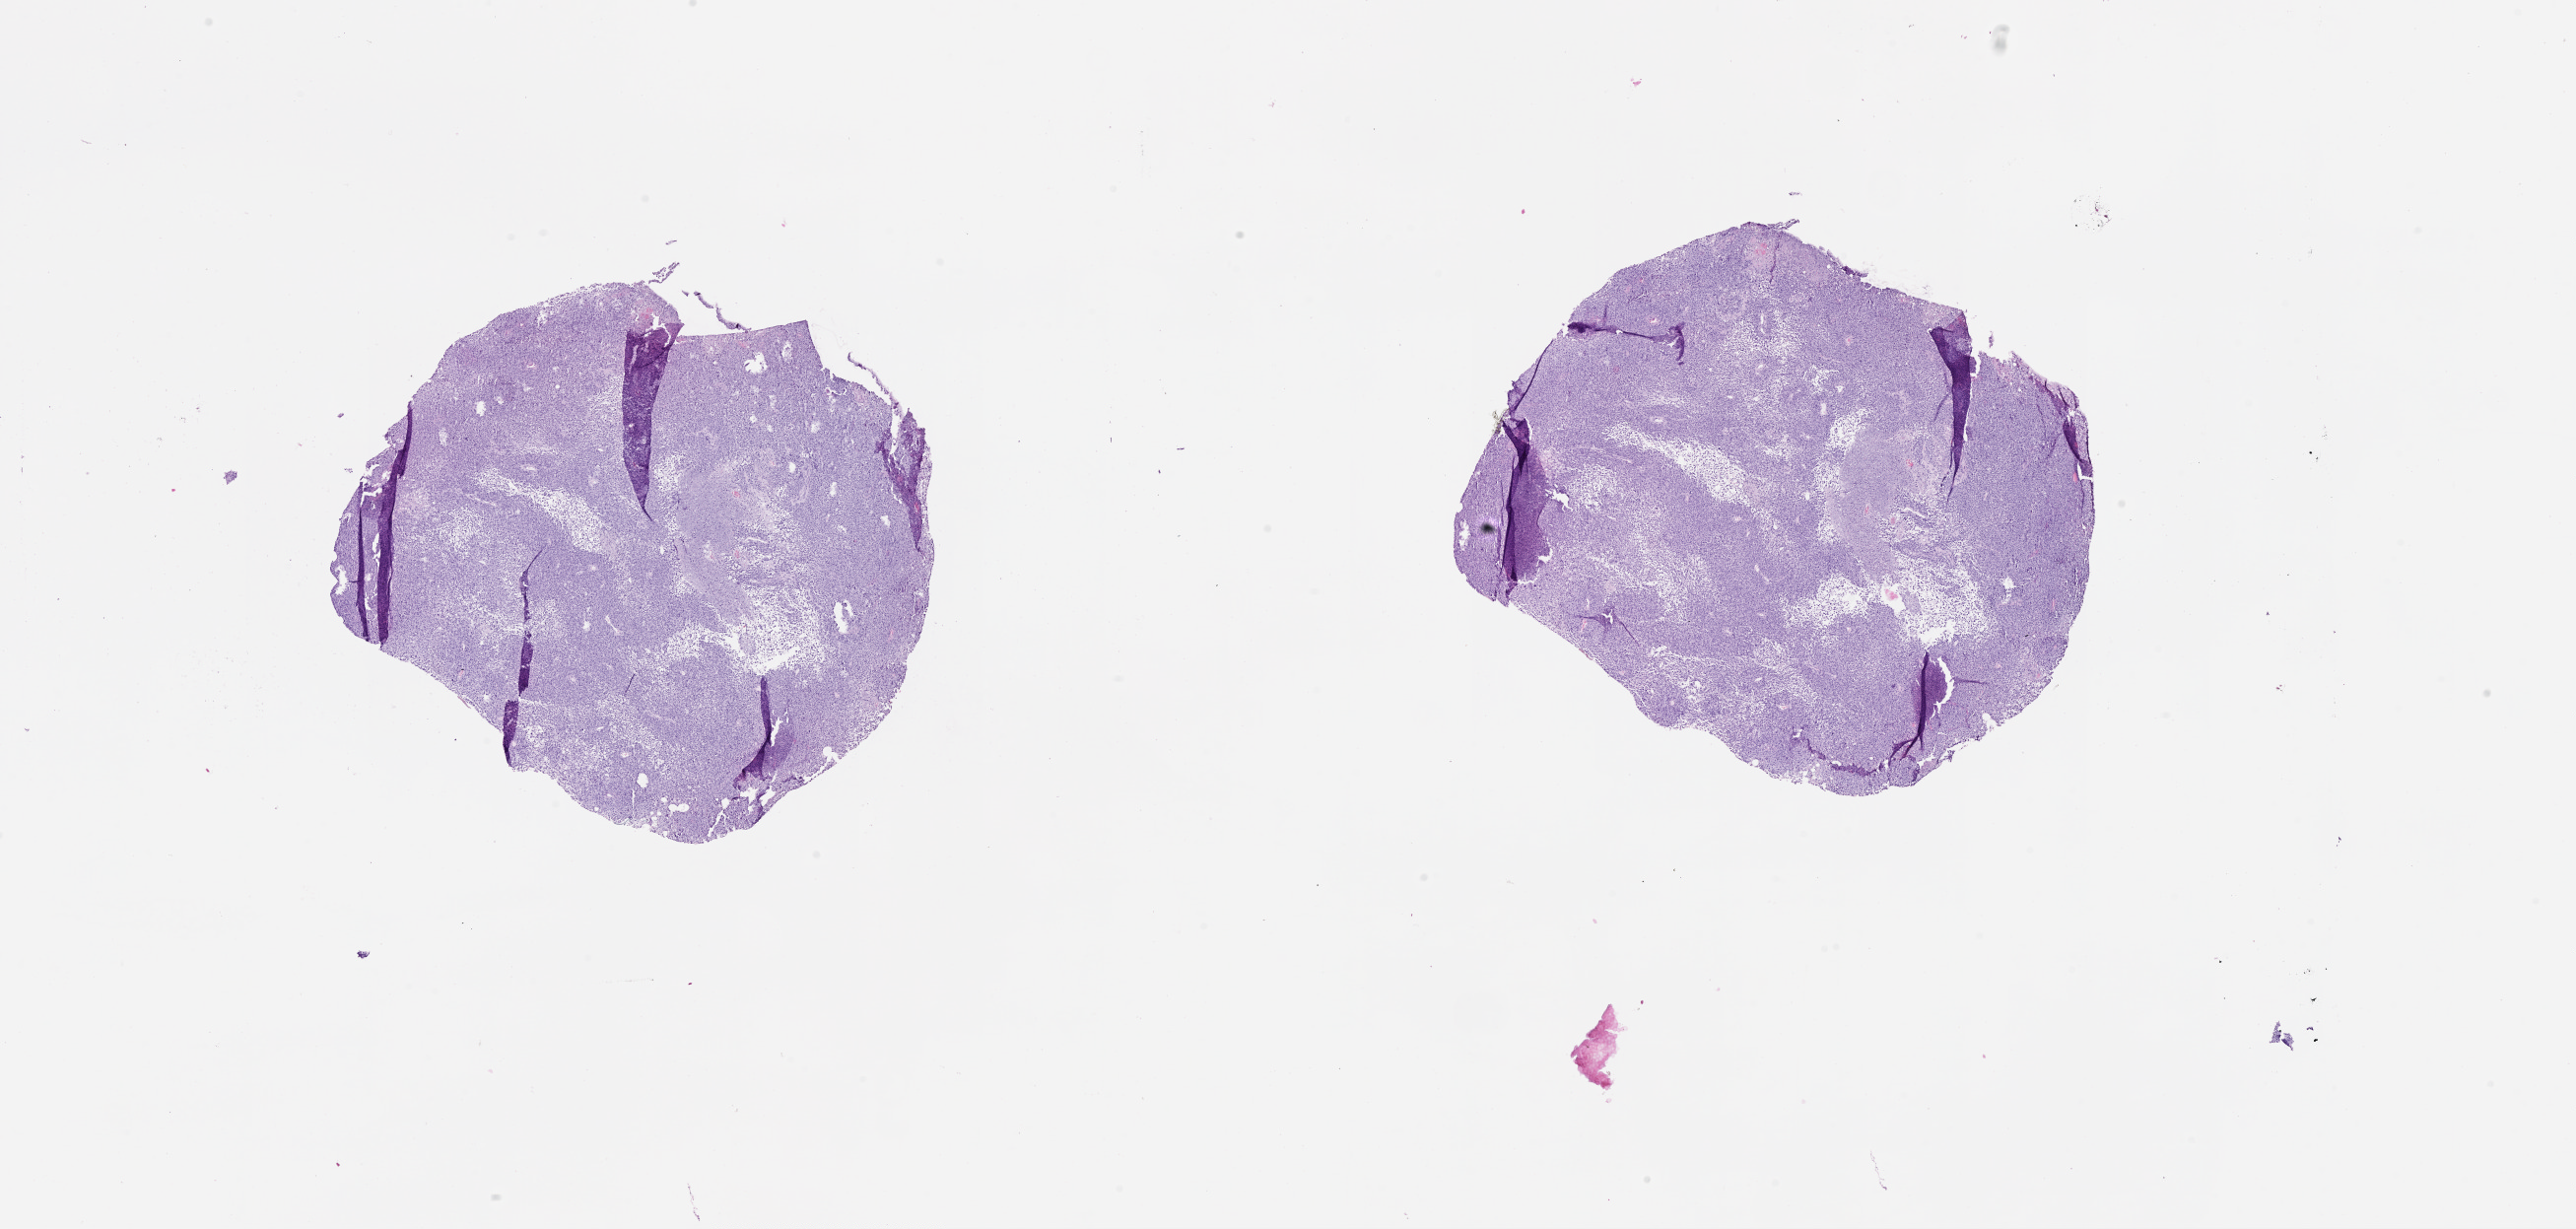
Whole-slide histology image, Hematoxylin and eosin (H&E) stained — whole scanned area (about 21.0 x 10.0 mm, slide scanned at 20x) shown as a low-resolution overview. Male, 72 y/o.
- patient diagnosis: Malignant melanoma, NOS